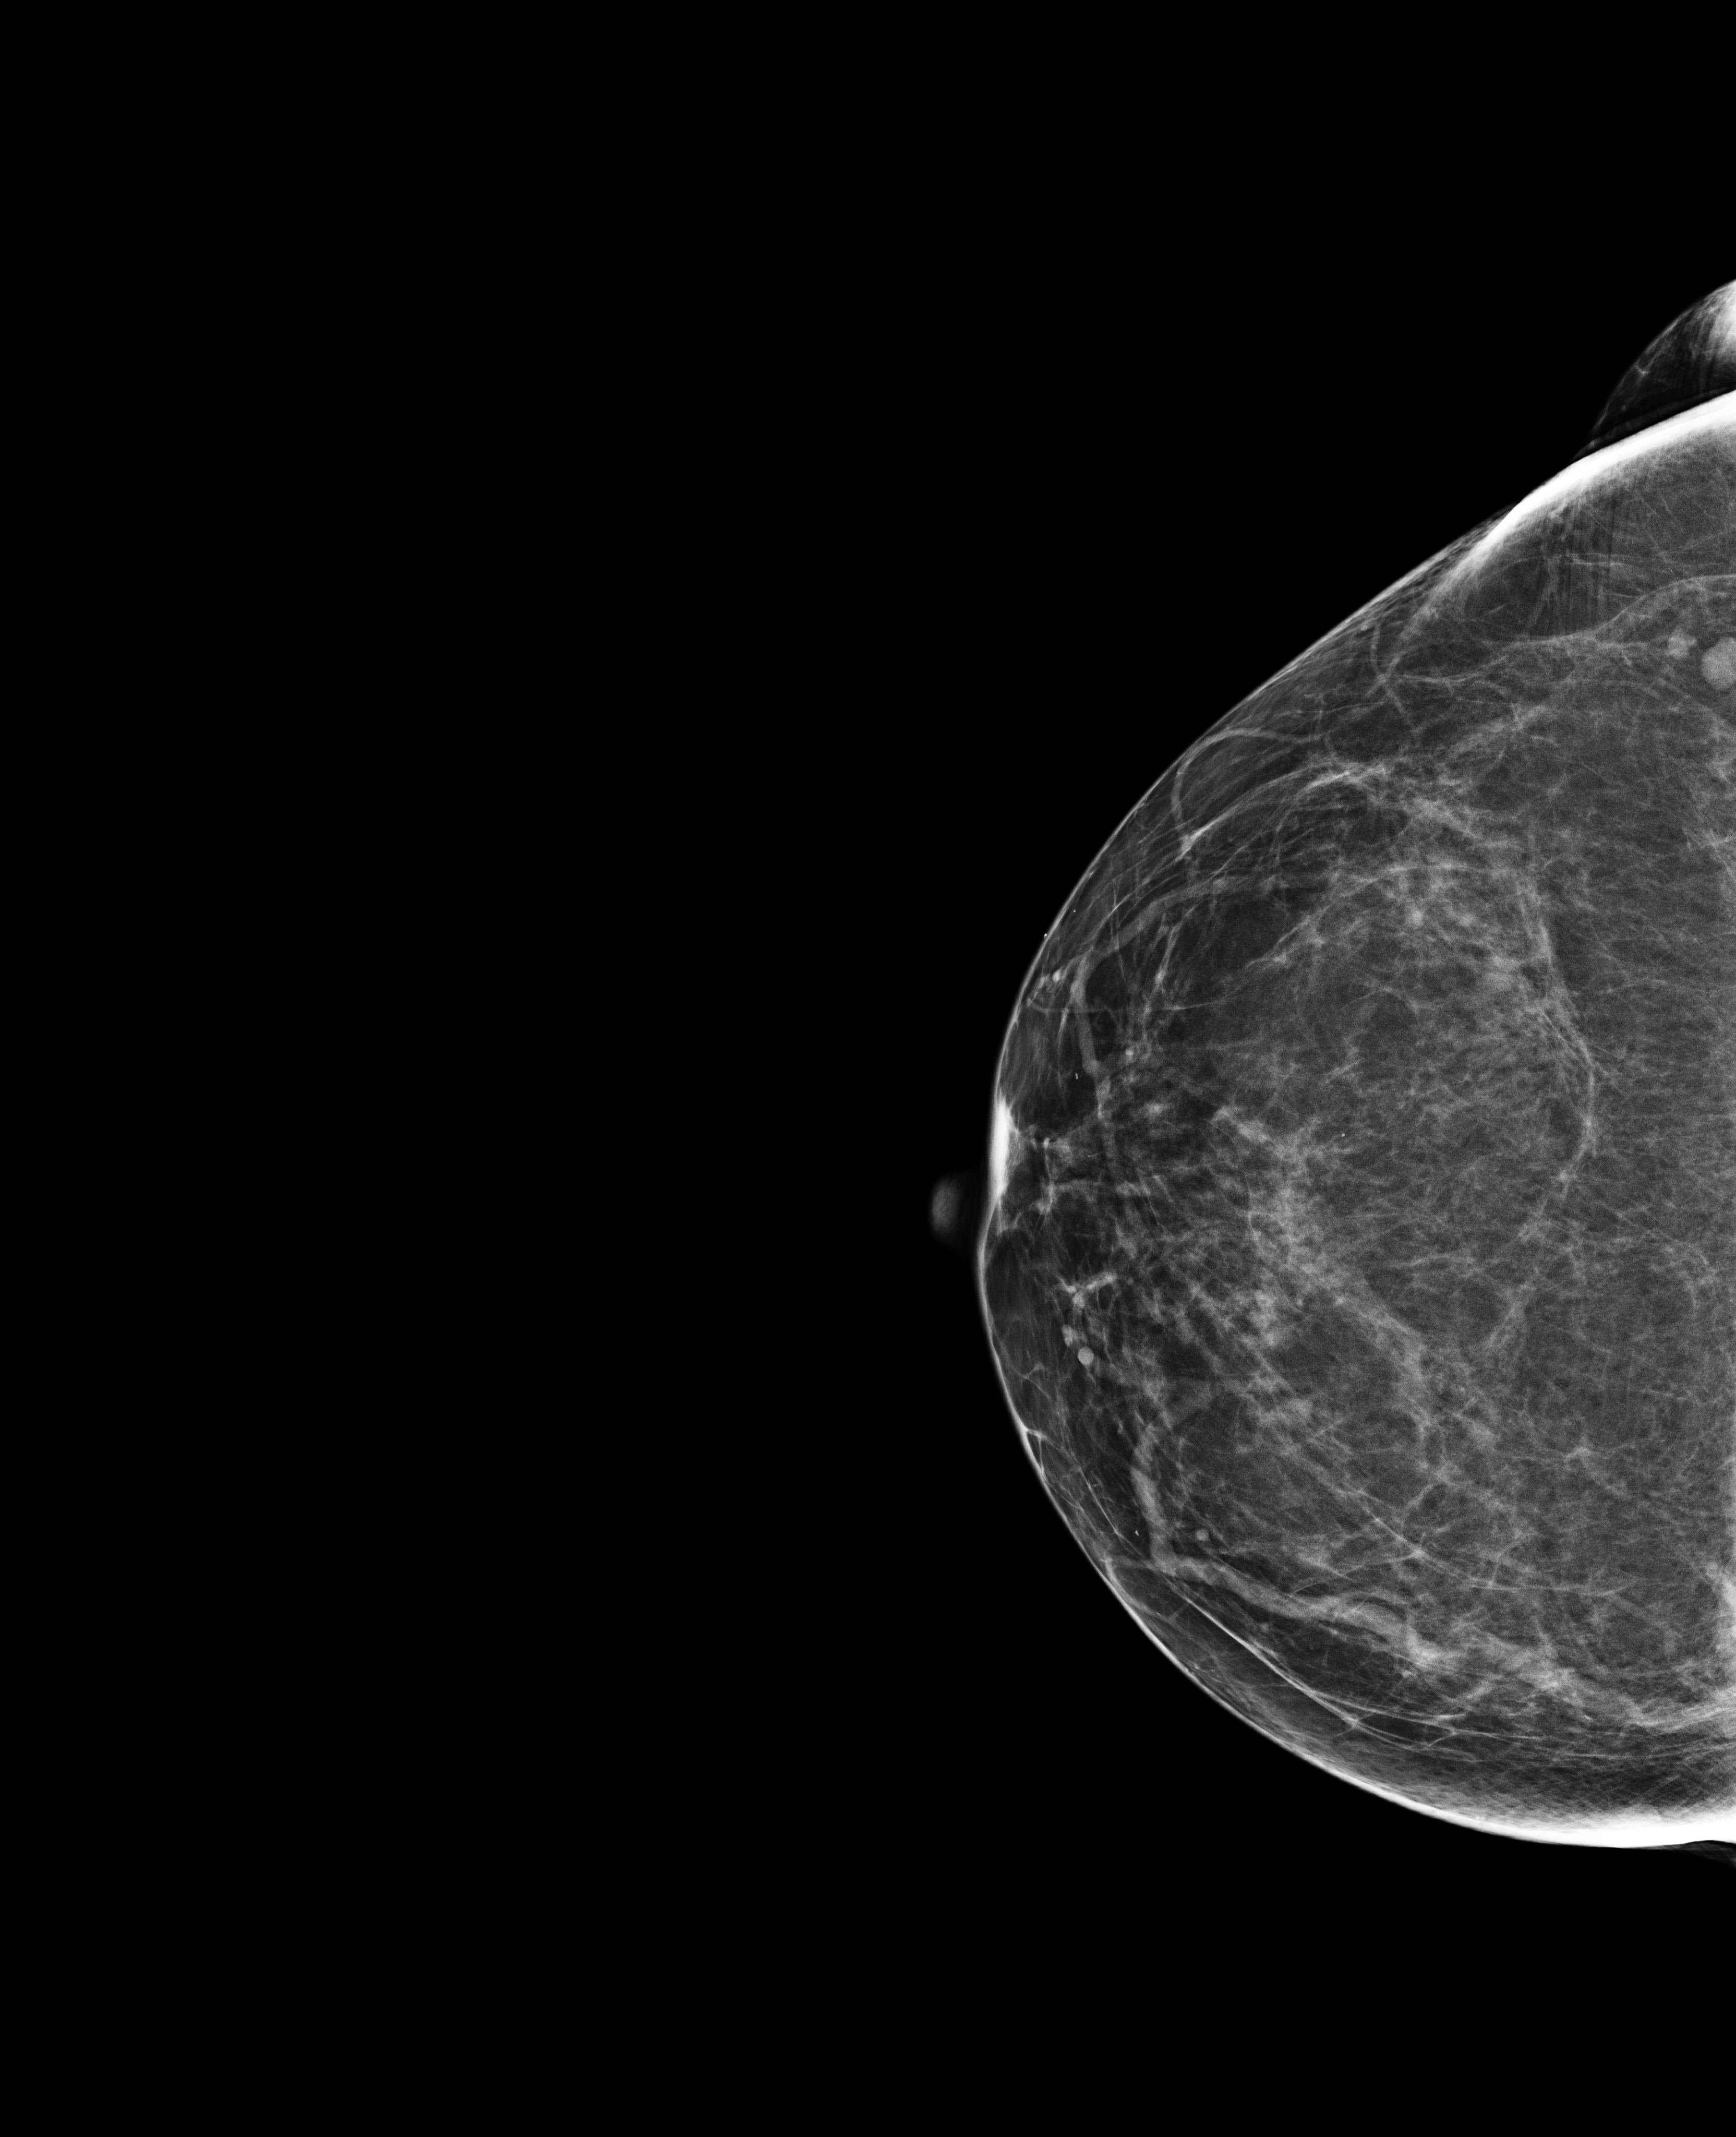
Digital mammogram (FFDM); right breast; CC view; annual screening mammography examination. Female patient, age 54 years.
Final BI-RADS assessment for this screening round (tomosynthesis exam, both breasts): category 2.